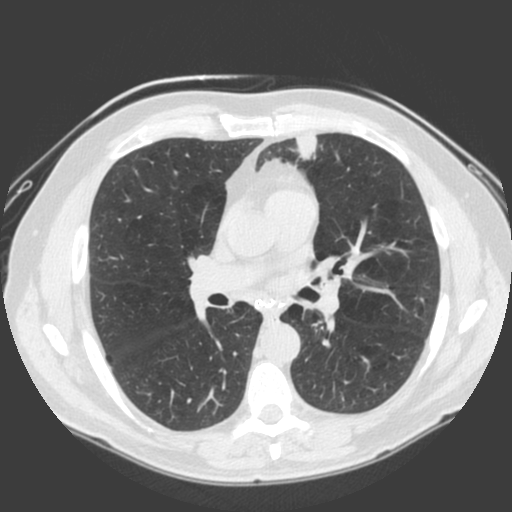
Low-dose screening chest CT, one axial slice. Slice 103 of 185 in the series (ordered by position). 120 kVp. Lung window (W 1500 / L -600 HU). 512 × 512 image matrix.
Annotated regions visible in this slice (manually delineated by an expert):
- lesion 1 (tumor, lower lobe of left lung): bounding box <293,135,321,161> (left, top, right, bottom; pixels)